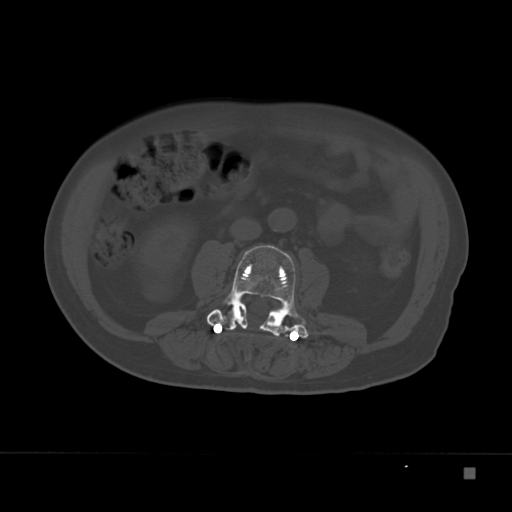
CT including the spine, one axial slice; position 66 of 332 along the scan axis; reconstruction kernel Br40s; 120 kVp; bone window (W 1800 / L 400 HU); 512 × 512 image matrix, field of view 389 × 389 mm. Patient: male, 72 years. From the clinical record (not read from this slice): primary cancer: skeletal.
Annotated regions visible in this slice (semi-automatically segmented with operator editing):
- L3 vertebra: bounding box [x1, y1, x2, y2] px = [207, 244, 309, 339]